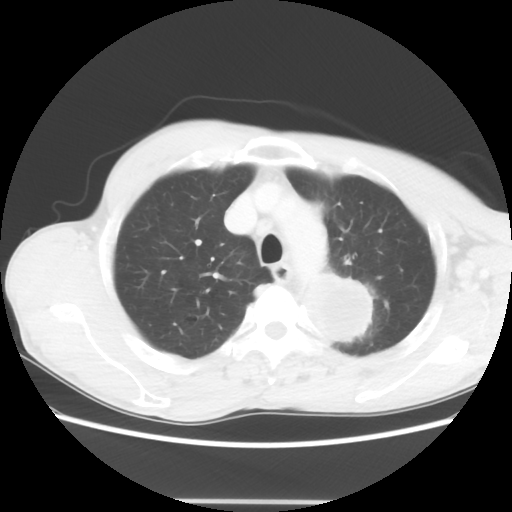
Chest CT, one axial slice; slice 51 of 62 in the series (ordered by position); lung window (W 1500 / L -600 HU); 5 mm slice thickness; 512 × 512 image matrix, field of view 360 × 360 mm. Patient: male, 61 years. From the clinical record (not read from this slice): clinical TNM (as recorded): T3 N1 M1.
Annotated regions visible in this slice (rectangle marked by the reading radiologist):
- lung tumour (recorded histology: adenocarcinoma): bounding box <300,274,392,354> (left, top, right, bottom; pixels)